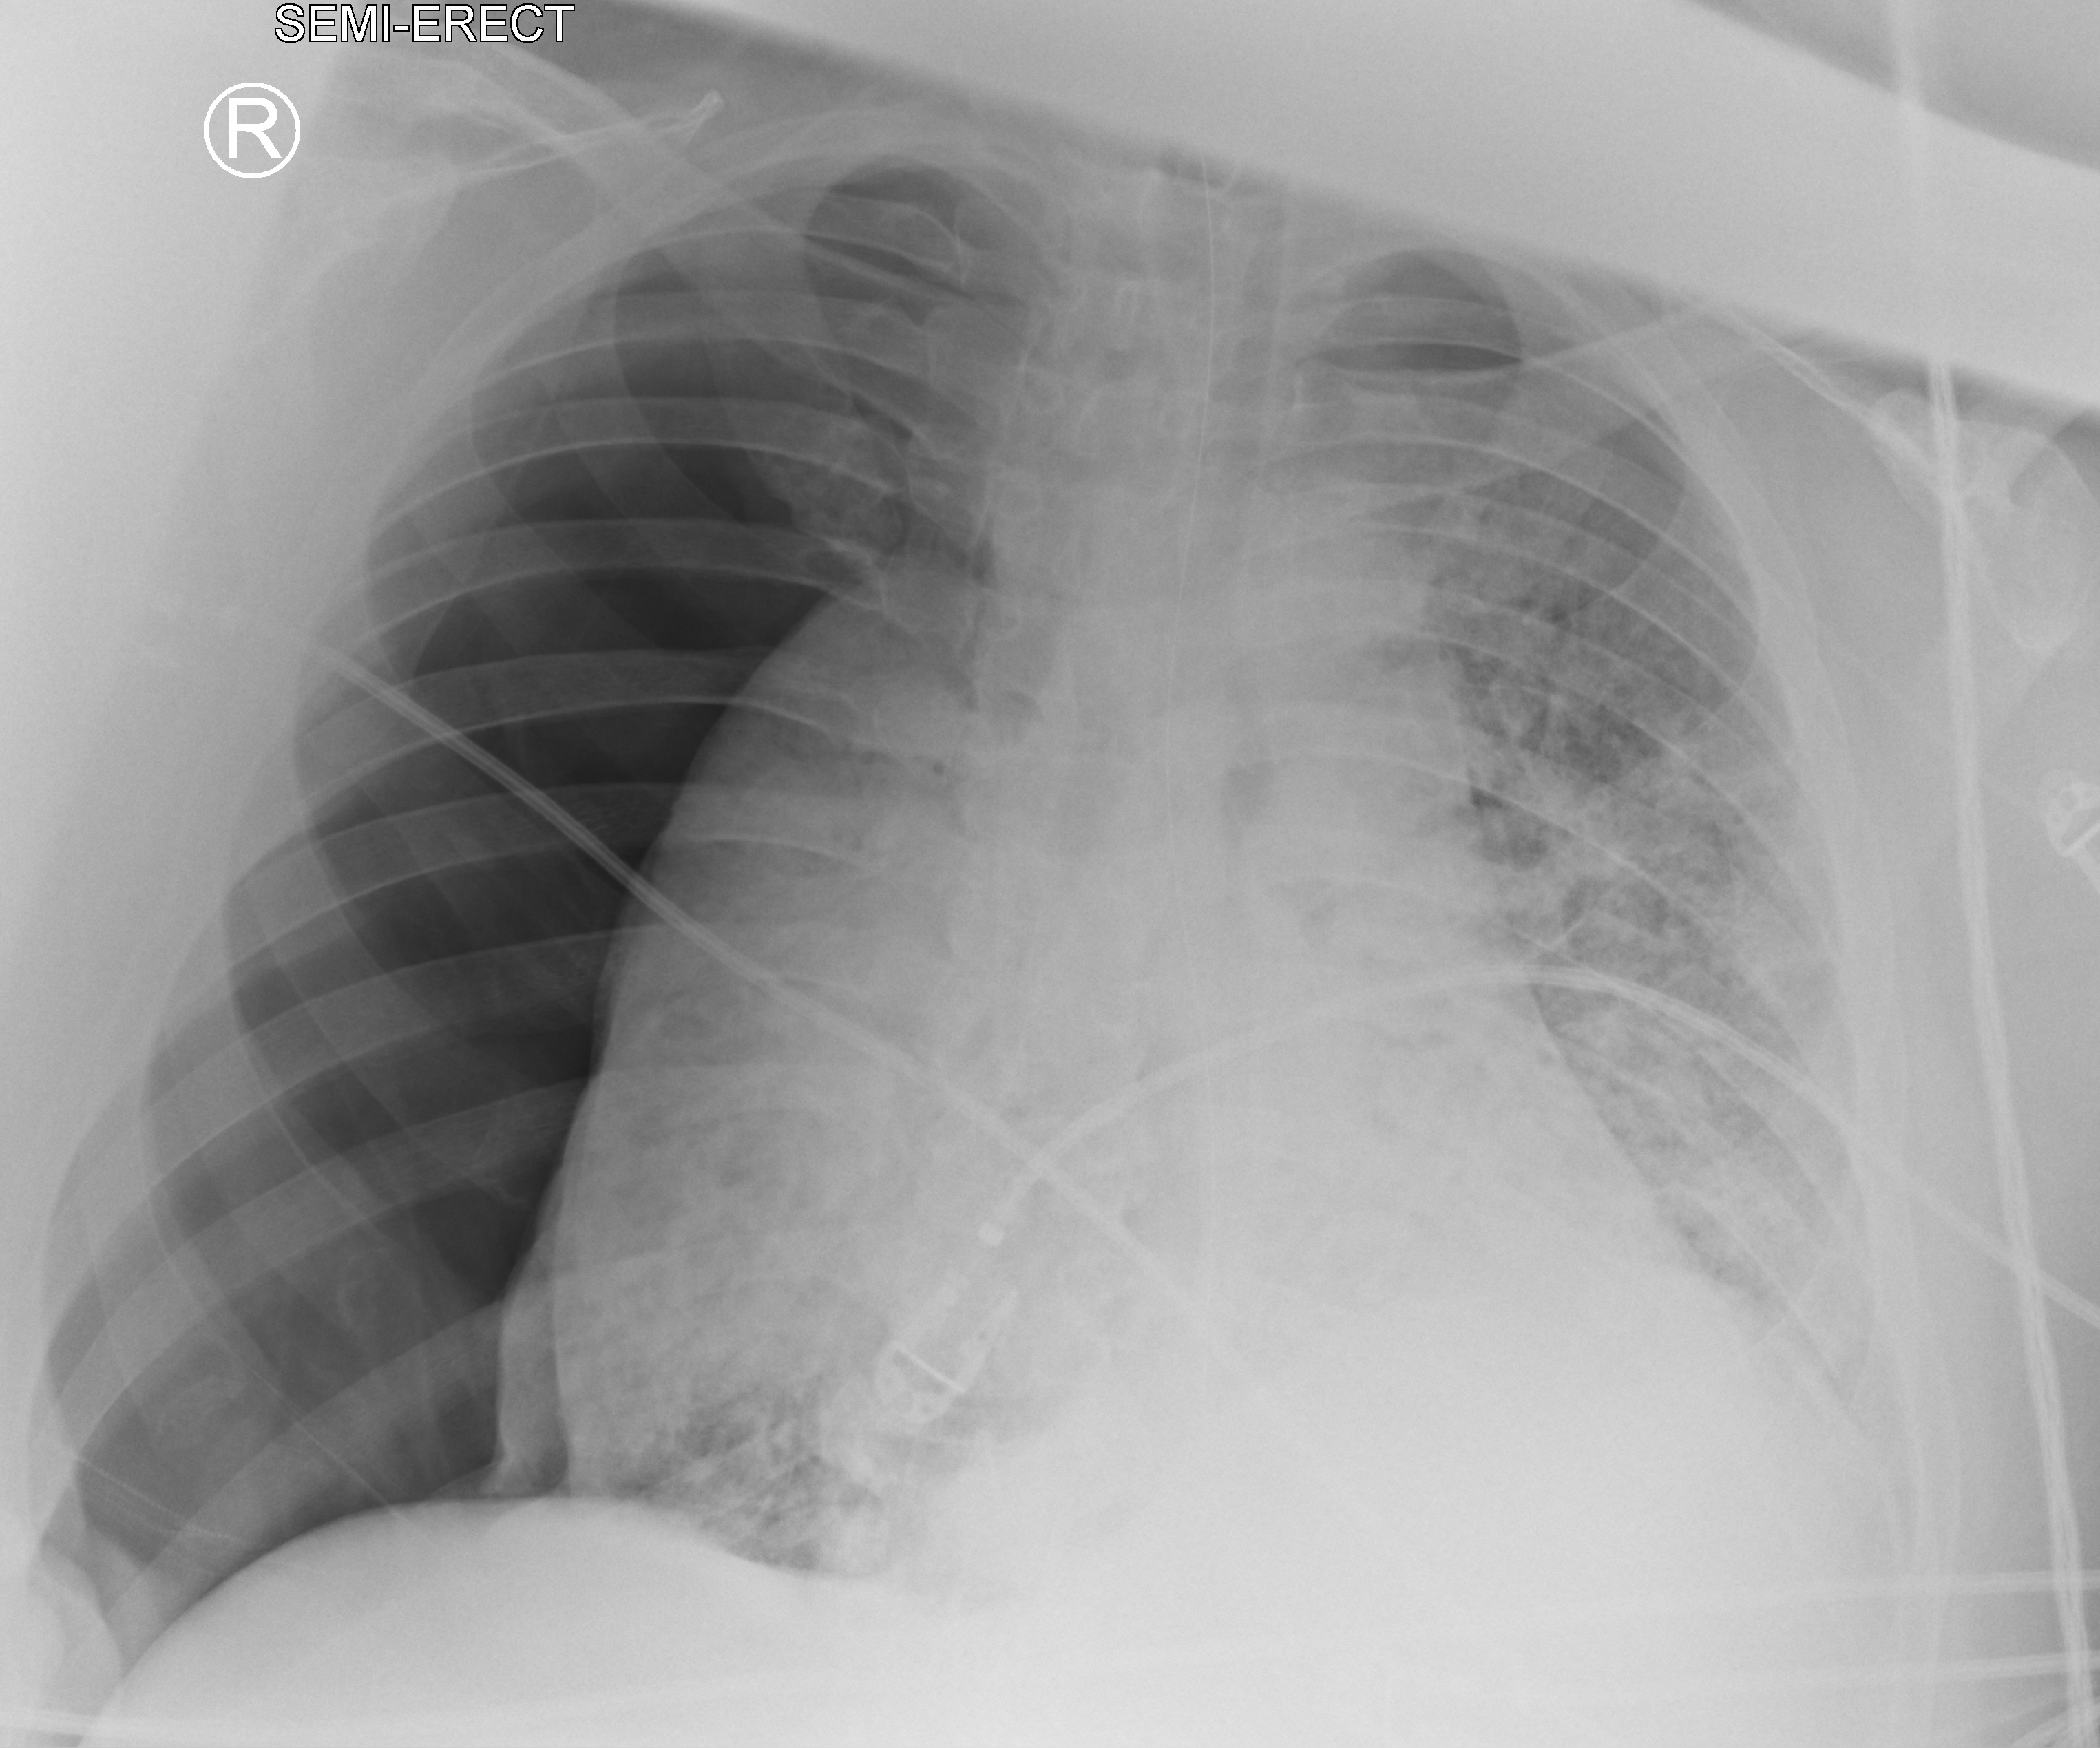
Chest X-ray (portable); anteroposterior (AP) projection. Patient hospitalised with COVID-19, aged 18–59 years.
Hospital-stay facts (about this admission, not read from this image; timing relative to this image not recorded):
- admitted to intensive care during this hospital stay: yes
- mechanically ventilated during this hospital stay: yes